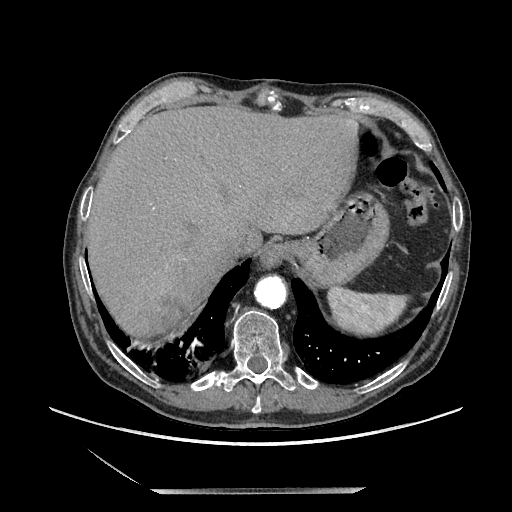
Contrast-enhanced abdominal CT, one axial slice; slice 179 of 243 in the series (ordered by position); soft-tissue window (W 400 / L 40 HU); 512 × 512 image matrix, field of view 420 × 420 mm. Male patient. Case-level facts recorded for this patient, not image findings: diagnosis: adrenocortical carcinoma; tumour side: right adrenal; tumour size at pathology: 16 cm; Ki-67 index: 17 %; stage (as recorded): 3.
Structures marked on this image (semi-automatically segmented with operator editing):
- mass: bounding box (x1, y1, x2, y2) in pixels: (152, 302, 183, 338)